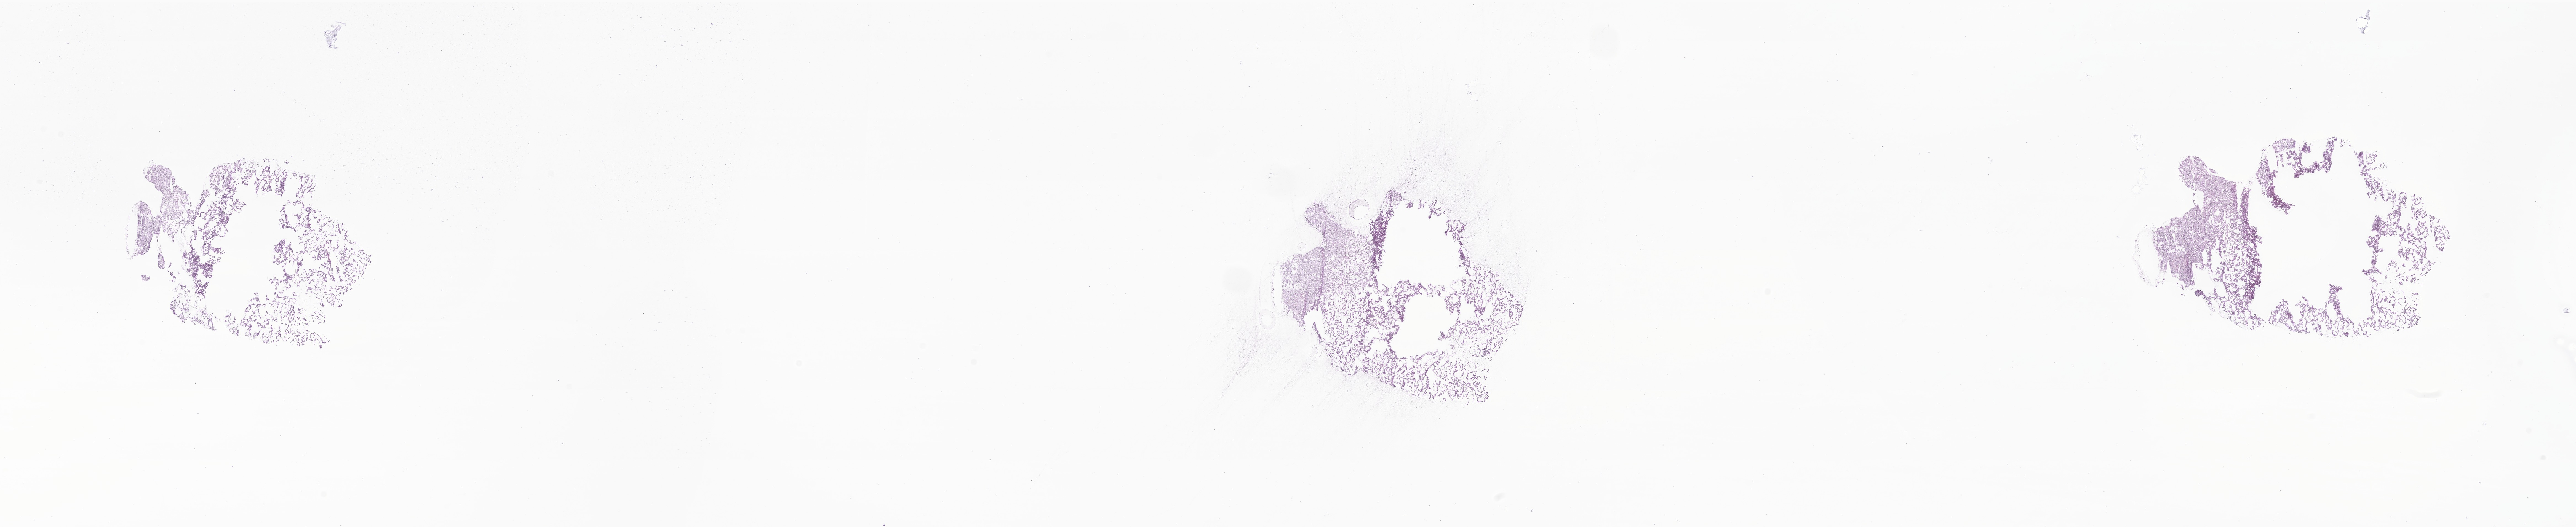
Whole-slide image, hematoxylin and eosin (H&E) stain of tumor tissue from the brain, a low-resolution overview of the entire scanned area, about 39.4 x 8.1 mm; cryosection (OCT / tissue freezing medium). Patient: female, age 170 days.
Recorded diagnosis: Choroid plexus carcinoma.